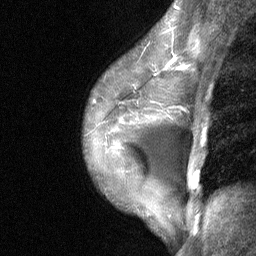
Breast MRI (dynamic contrast-enhanced), one sagittal slice. Slice 48 of 64 in the series (ordered by position). Dynamic contrast-enhanced study with each time point stored as its own series, time point 2 of 3 at this slice position (early post-contrast, ordered by acquisition time). 1.5 T. TE 4.8 ms, TR 27 ms. 2 mm slice thickness. 256 × 256 image matrix, field of view 180 × 180 mm. Female patient, age 35 years. Case-level facts recorded for this patient, not image findings: setting: breast cancer imaged before/during neoadjuvant chemotherapy; receptor status: HR-positive, HER2-negative.
Structures marked on this image (semi-automatic segmentation, software-assisted and operator-edited):
- analysis volume of interest (the breast-tissue region the enhancement analysis was run in; not a lesion): bounding box [x1, y1, x2, y2] px = [84, 58, 188, 171]
- tumour enhancement mask (voxels above the 90 % enhancement threshold inside the analysis volume of interest): [176, 67, 180, 69]